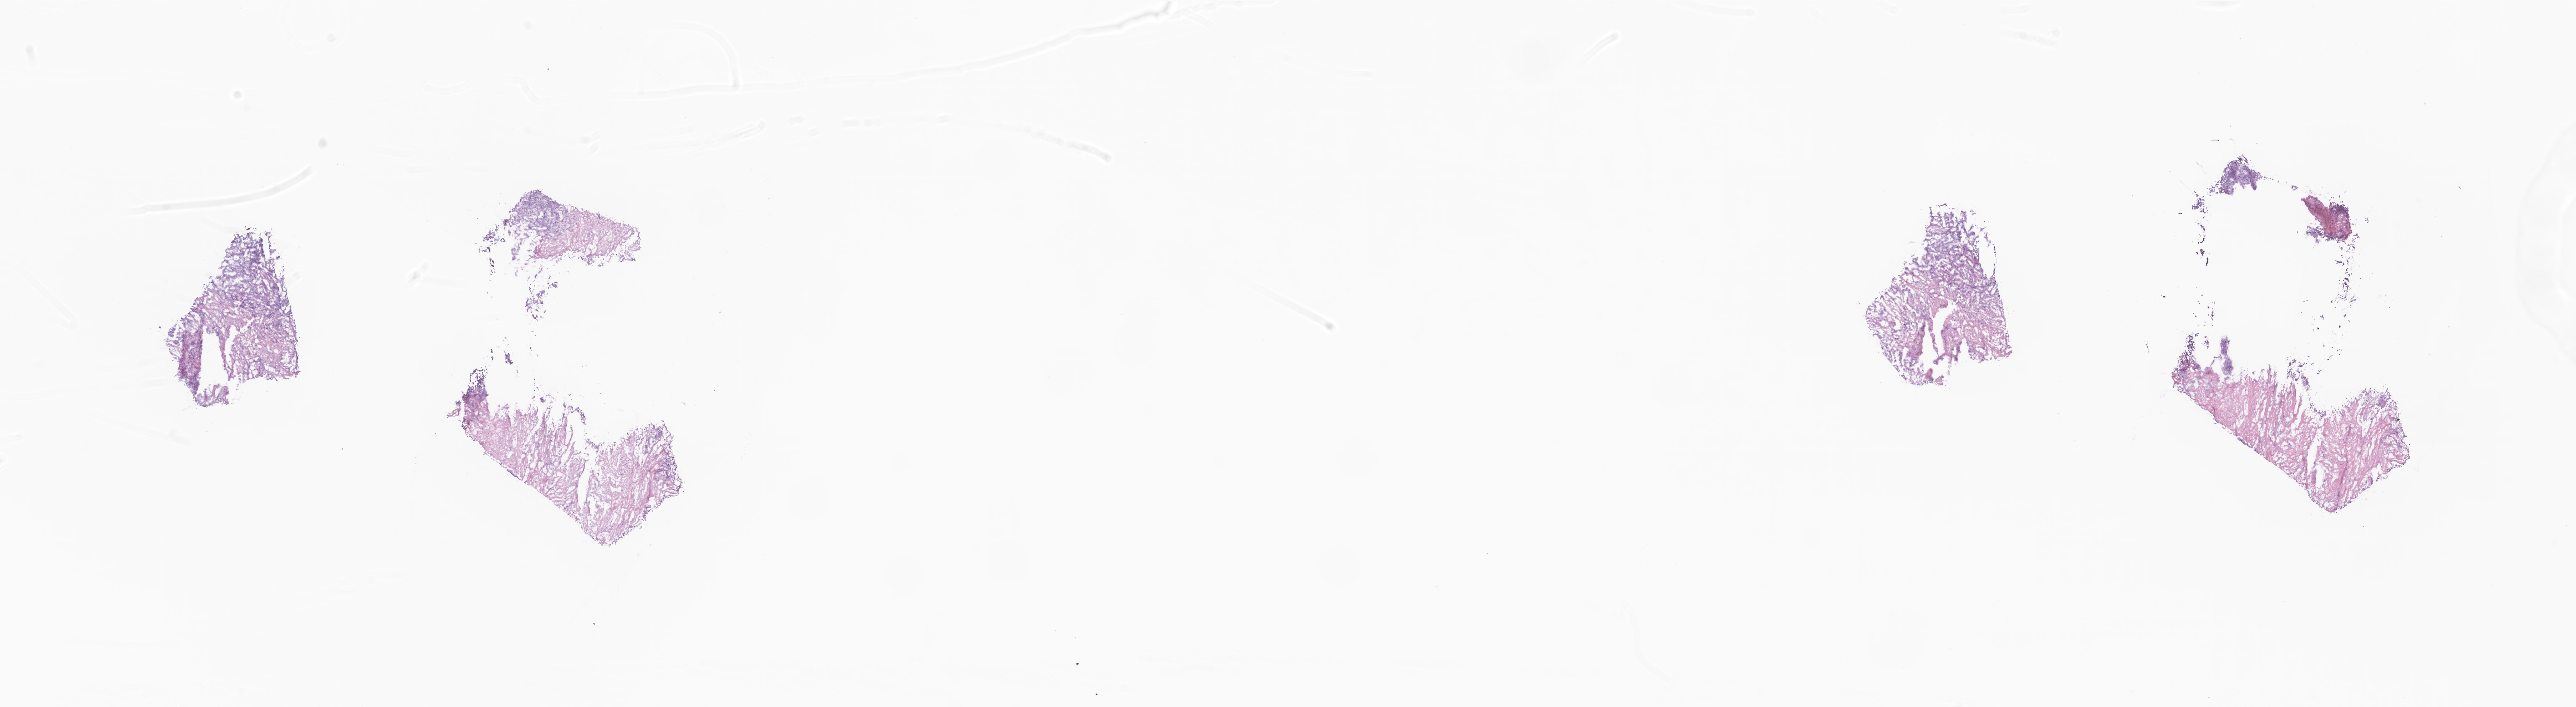
Haematoxylin and eosin whole-slide image — low-resolution overview of the scanned area, about 30.4 x 8.4 mm; cryosection; primary tumor; site: breast. Female, age 53 years at initial diagnosis. Slide review estimates, as recorded: tumor cells 40%, tumor nuclei 50%, stromal cells 30%, necrosis 0%, normal cells 30%. Infiltration values recorded for this section: lymphocyte infiltration 0%, monocyte infiltration 0%, neutrophil infiltration 0%.
Section: bottom of the tissue portion. Histologic diagnosis: Infiltrating duct carcinoma, NOS.